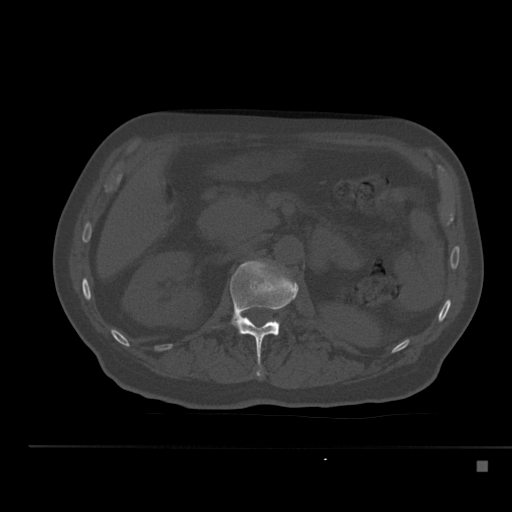
CT including the spine, one axial slice. Slice 205 of 517 in the series (ordered by position). Reconstruction kernel Br40s. Bone window (W 1800 / L 400 HU). 1.5 mm slice thickness. 512 × 512 image matrix, field of view 408 × 408 mm. Patient: male, 70 years. From the clinical record (not read from this slice): primary cancer: renal; vertebrae with lytic lesions (as recorded): T4, T6, T10, T12, L3, L4, L5.
Annotated regions visible in this slice (semi-automatic segmentation, software-assisted and operator-edited):
- L1 vertebra: bounding box [x1, y1, x2, y2] px = [214, 259, 299, 376]